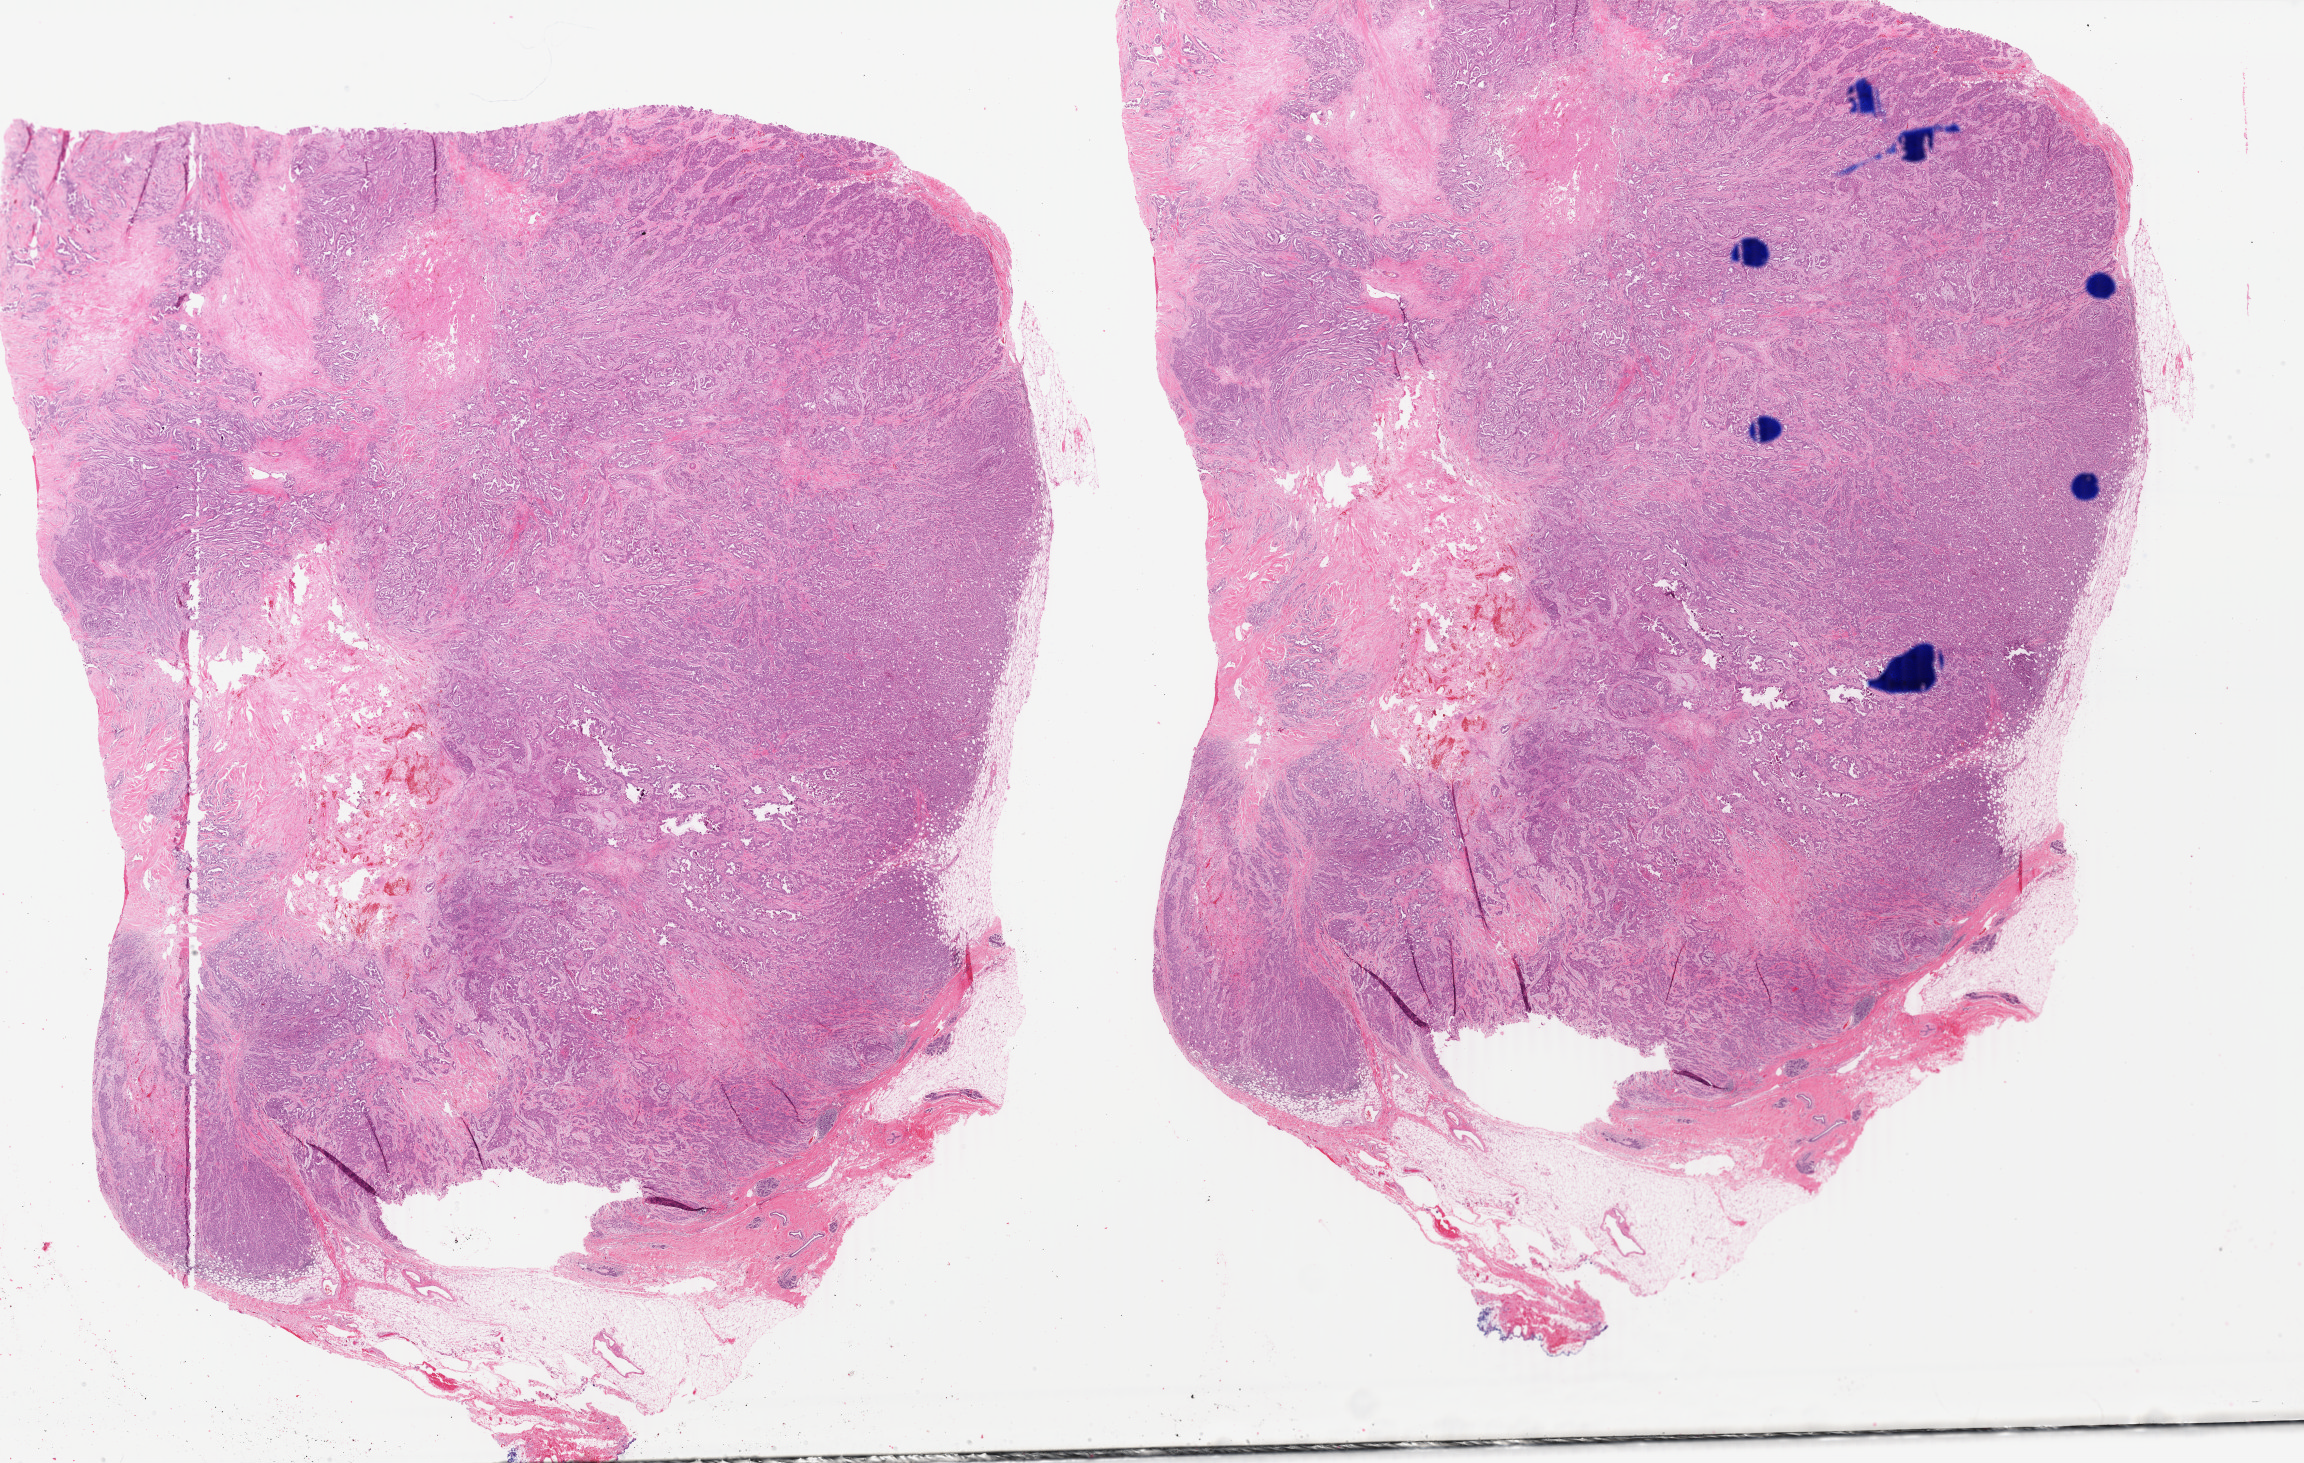
Digitized H&E-stained tissue section (whole slide), a low-resolution overview of the entire scanned area, about 36.6 x 23.3 mm (from a 40x scan). Formalin-fixed paraffin-embedded (FFPE) diagnostic section. Primary tumour sample from the breast. Female patient; age at initial diagnosis 26 years.
Pathologic diagnosis: Infiltrating duct carcinoma, NOS.